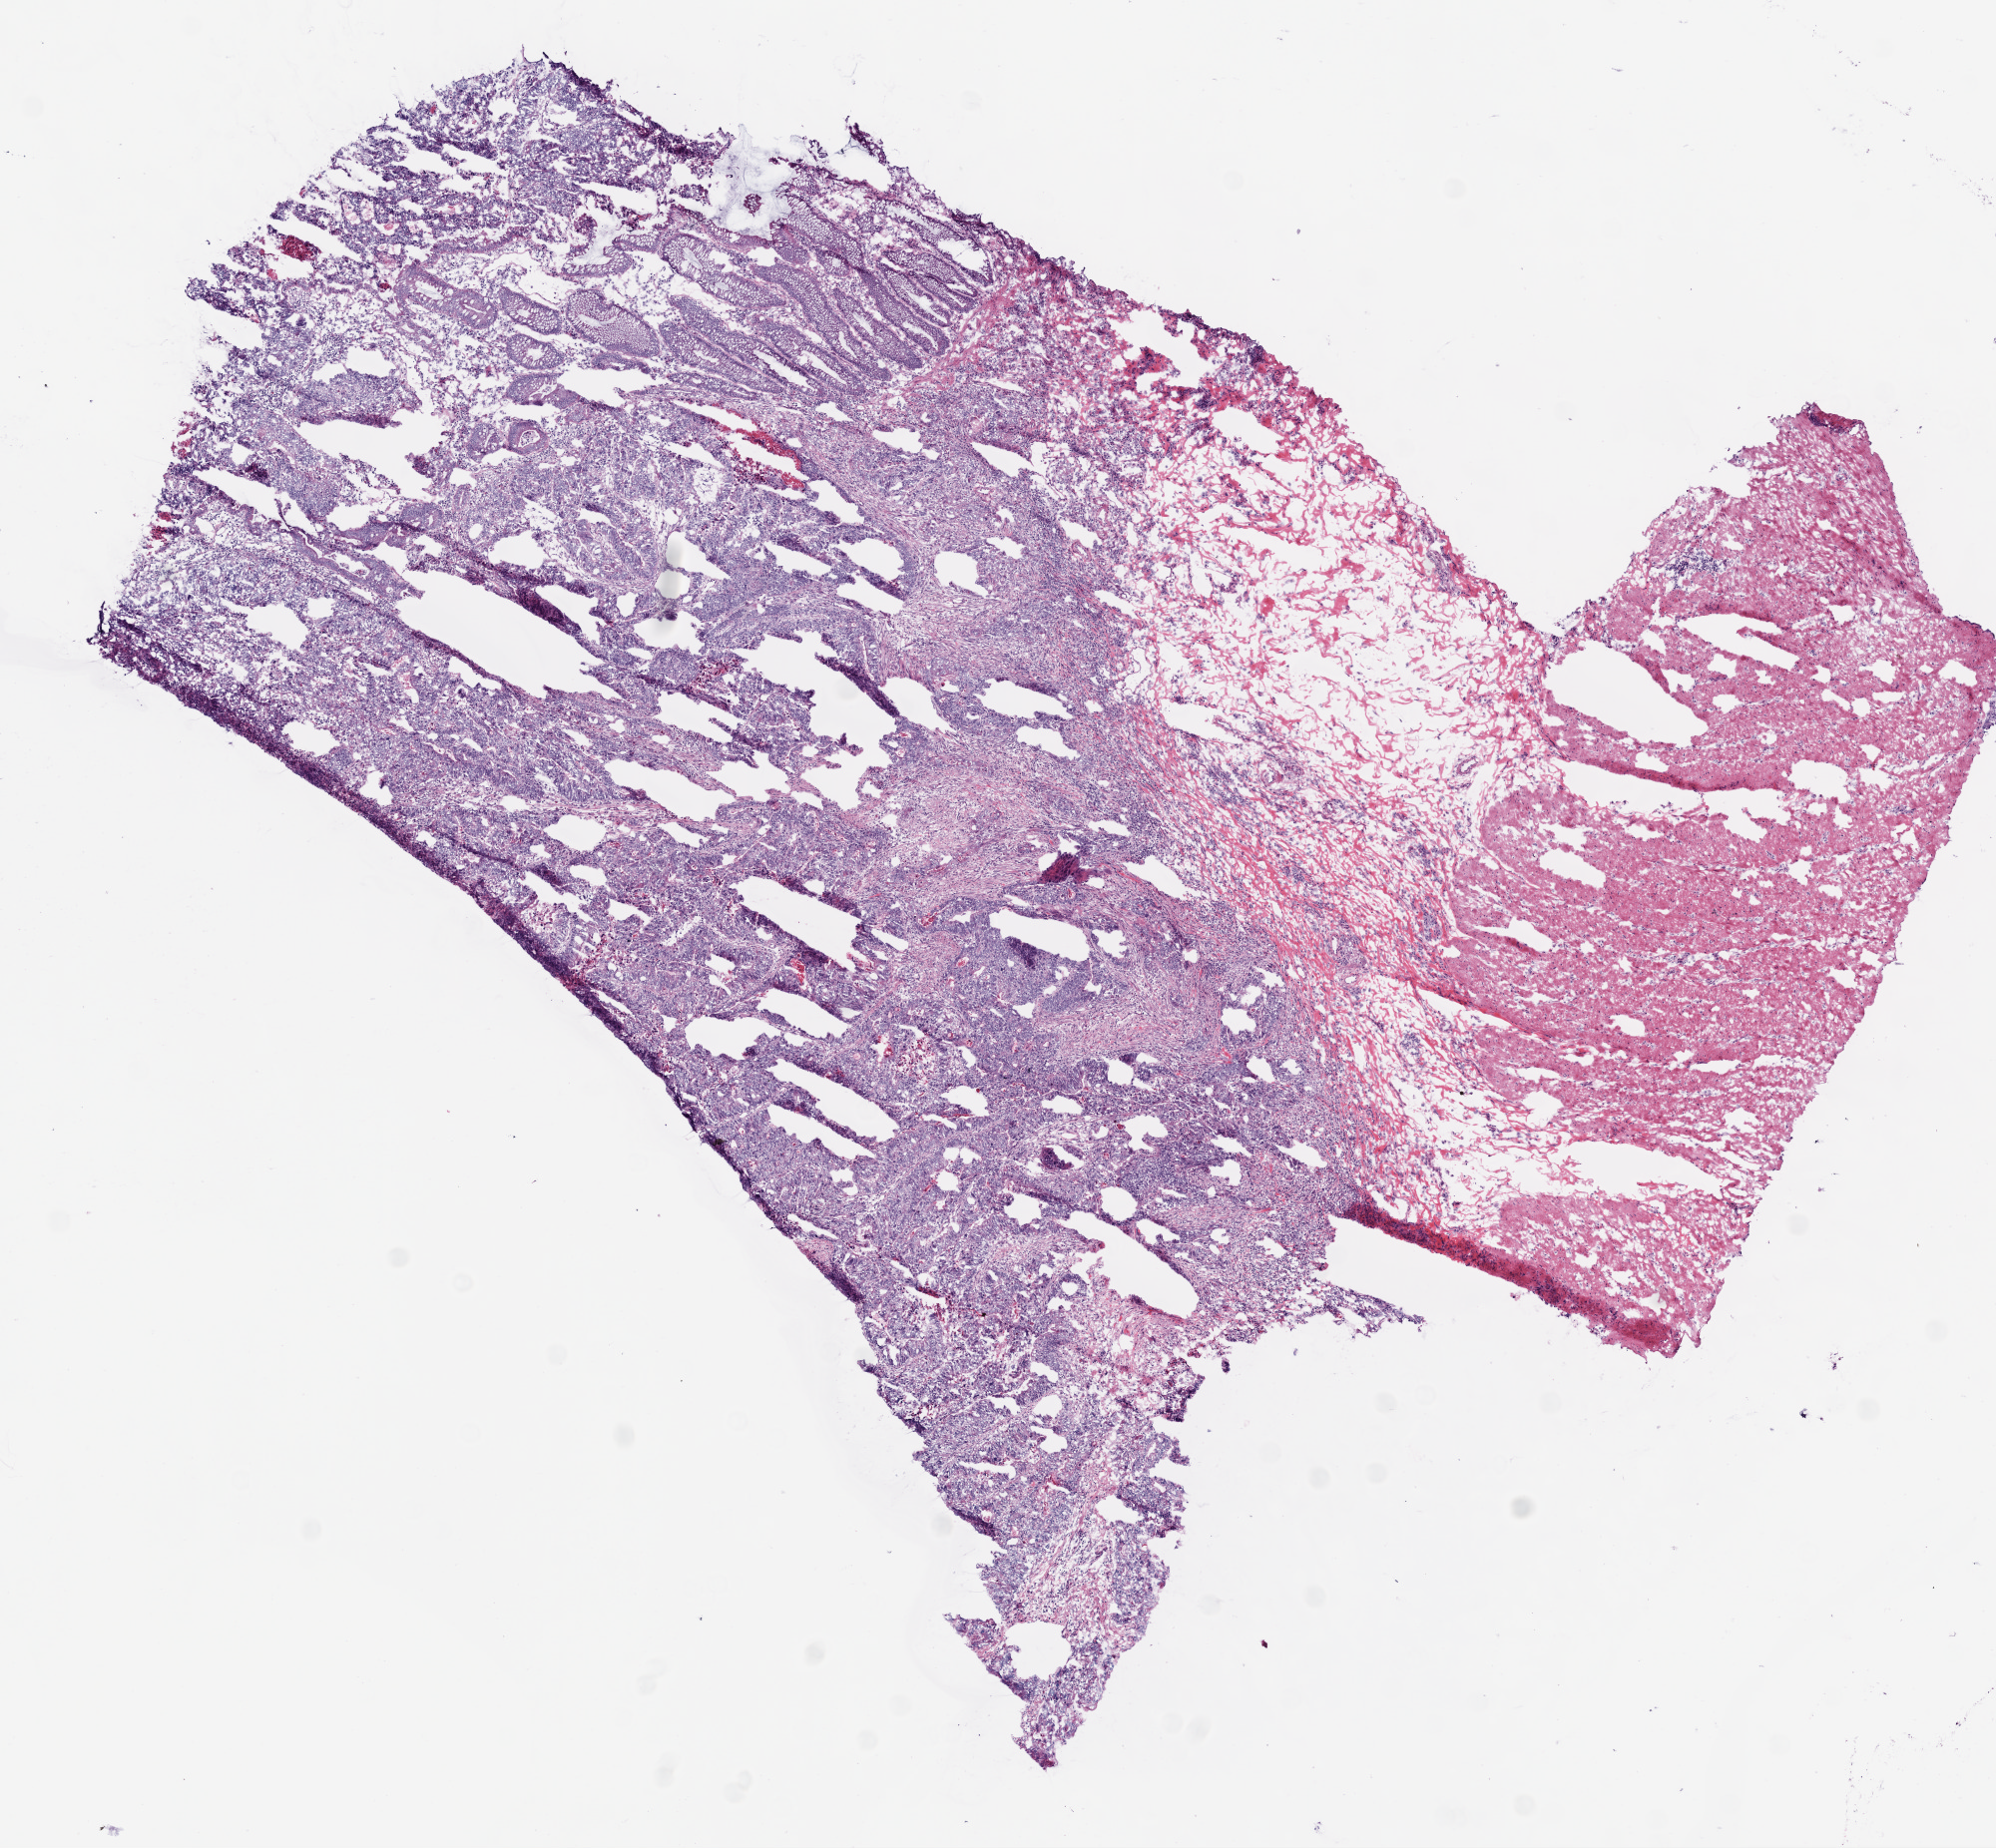
Digitized H&E-stained tissue section (whole slide), shown as a low-resolution overview of the whole scanned area (about 8.0 x 7.4 mm, slide scanned at 20x); frozen section; sample: primary tumour, colon. Female, age 61 years at initial diagnosis. Pathologist review of this section (percent, as recorded): tumour cells 50%, tumour nuclei 60%, normal cells 0%, stromal cells 50%, necrosis 0%.
Pathologic diagnosis: Adenocarcinoma, NOS. AJCC pathologic stage: I (6th edition). Lymph nodes positive (case pathology): 0 of 21 examined.